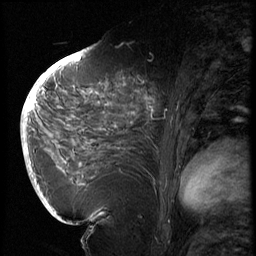
Breast MRI (dynamic contrast-enhanced), one sagittal slice; slice 35 of 72 in the series (ordered by position); 3 images stored at this slice position (order not interpretable as contrast timing); 1.5 T; TE 4.2 ms, TR 8.9 ms; 2.5 mm slice thickness; 256 × 256 image matrix, field of view 200 × 200 mm. Female patient, age 56 years. Case-level facts recorded for this patient, not image findings: setting: breast cancer imaged before/during neoadjuvant chemotherapy.
Outlined on this slice (semi-automatic segmentation, software-assisted and operator-edited):
- analysis volume of interest (the breast-tissue region the enhancement analysis was run in; not a lesion): bounding box <114,76,177,138> (left, top, right, bottom; pixels)
- tumour enhancement mask (voxels above the 140 % enhancement threshold inside the analysis volume of interest): <145,96,154,117>